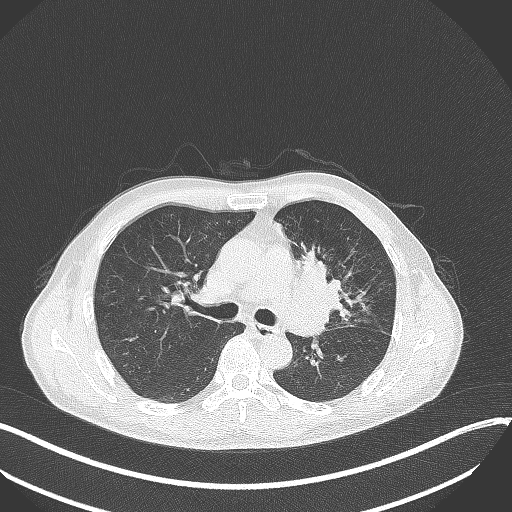
Chest CT, one axial slice. Position 208 of 411 along the scan axis. 120 kVp. Lung window (W 1500 / L -600 HU). 1 mm slice thickness. 512 × 512 image matrix, field of view 400 × 400 mm. Male patient, age 56 years. From the clinical record (not read from this slice): clinical TNM (as recorded): T2a N0 M0.
Structures marked on this image (rectangle marked by the reading radiologist):
- lung tumour (recorded histology: squamous cell carcinoma): bounding box (x1, y1, x2, y2) in pixels: (290, 242, 350, 323)